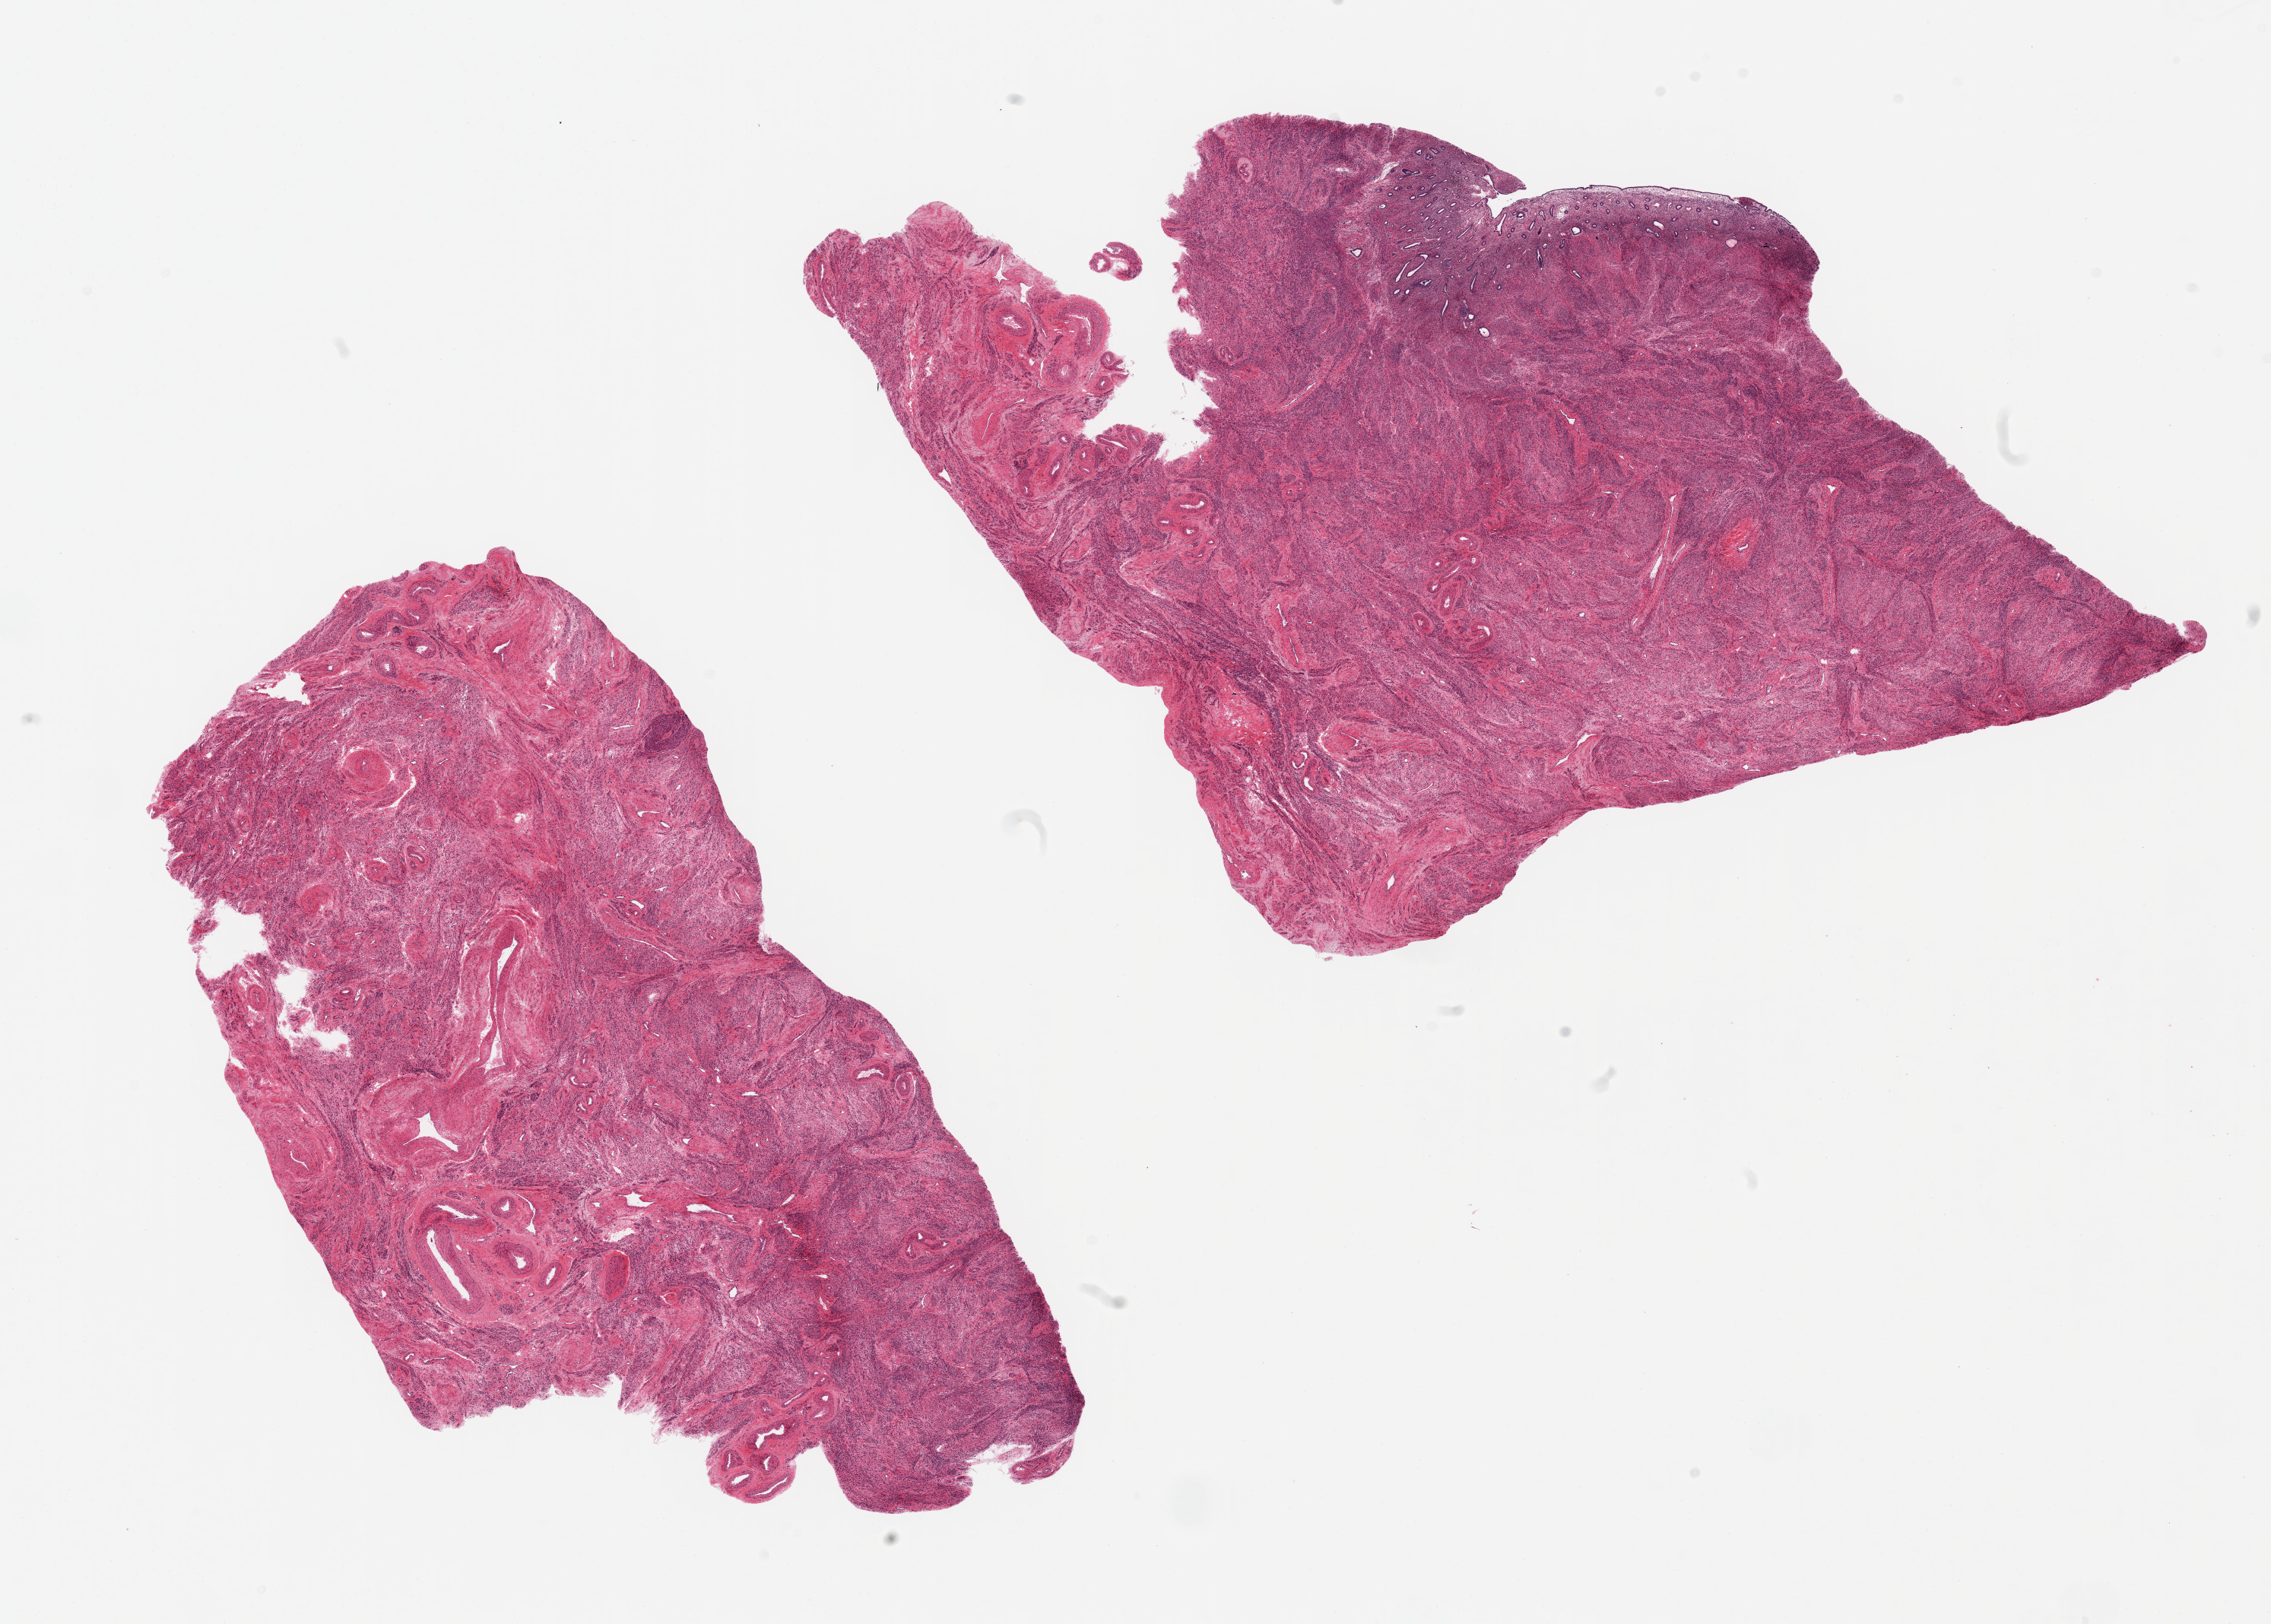
Whole-slide image, H&E stain, brightfield, whole scanned area (about 23.6 x 16.9 mm, slide scanned at 20x) shown as a low-resolution overview; PAXgene-fixed paraffin-embedded (PFPE) section; section of uterus (target tissue); tissue donor sample.
Review note (as recorded): 2 pieces, mainly myometrium; ~3x2mm focus of basal endometrium, well - preserved.